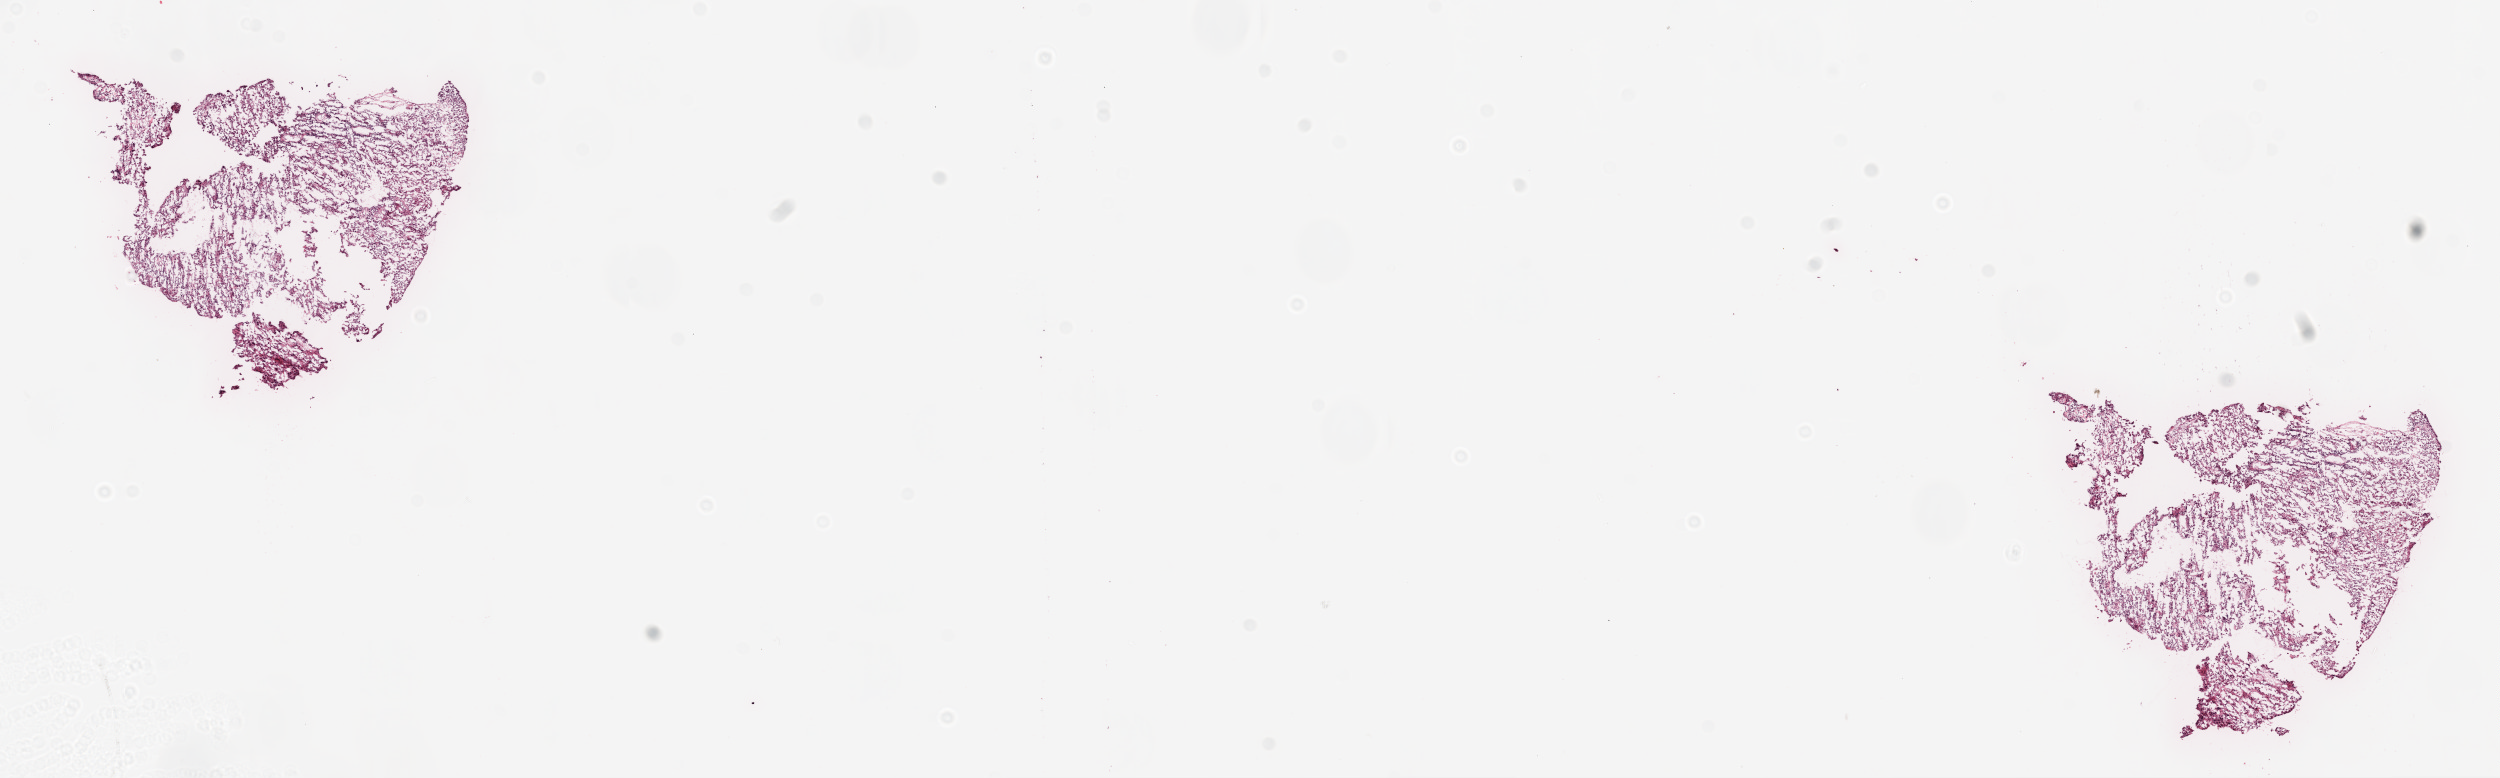
Whole-slide histology image, Hematoxylin and eosin (H&E) stained — shown as a low-resolution overview of the whole scanned area (about 20.1 x 6.2 mm, acquisition: 20x scan), frozen section from the top of the tissue portion, primary tumour sample from the brain. Male patient; age at initial diagnosis 48 years. Composition of this section per pathologist review: tumour cells 100%, tumour nuclei 85%, normal cells 0%, stromal cells 0%, necrosis 0%.
• pathologic diagnosis: Glioblastoma